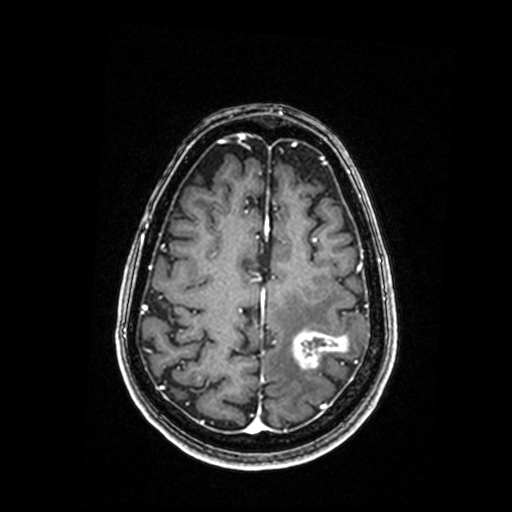
Brain MRI from a brain-tumour surgery series, one axial slice; T1-weighted post-contrast; 512 × 512 image matrix. From the clinical record (not read from this slice): histopathology: Metastastic Carcinoma, Poorly Differentiated; tumour location: Left Parietal.
Outlined on this slice (expert manual segmentation):
- tumour: box from (x=293, y=332) to (x=348, y=368) px